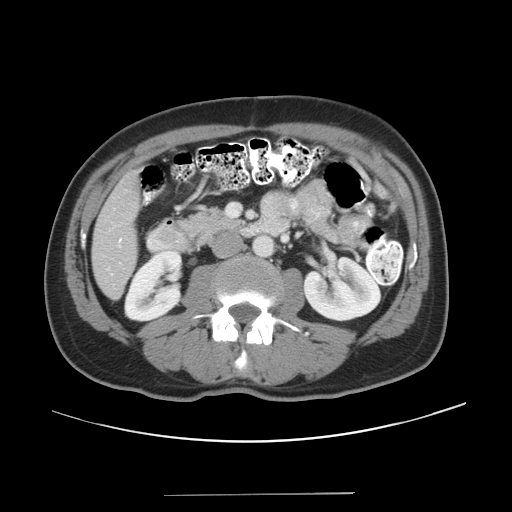
Contrast-enhanced abdominal CT, one axial slice; position 12 of 43 along the scan axis; reconstruction kernel STANDARD; intravenous contrast given; soft-tissue window (W 400 / L 40 HU); 5 mm slice thickness; 512 × 512 image matrix, field of view 409 × 409 mm. Male patient, age 65 years. From the clinical record (not read from this slice): diagnosis: colorectal cancer liver metastases, imaged before liver resection; multiple liver metastases: no; largest metastasis: 3.8 cm.
Outlined on this slice (outlined manually by an expert reader):
- liver: bounding box <94,175,140,297> (left, top, right, bottom; pixels)
- planned liver remnant (the part of the liver to remain after resection): <93,175,140,297>